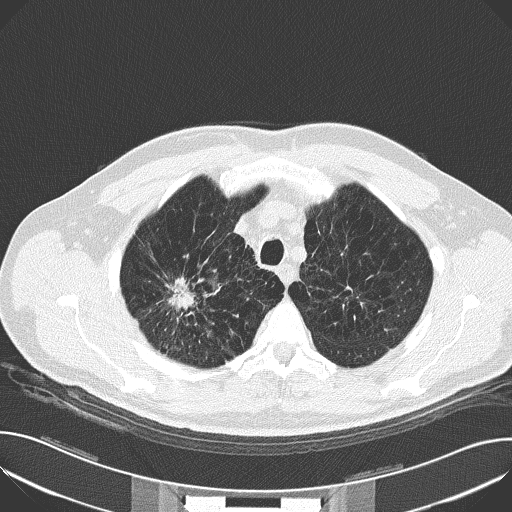
Axial slice from a low-dose chest CT screening exam; baseline annual screen; lung window (W 1500 / L -600 HU); 2 mm slice thickness; 120 kVp; slice 27 of 159 in the series; 512 × 512 image matrix, field of view 380 × 380 mm. Male participant, aged 59 years at enrolment.
• Expert-annotated lung lesion, bounding box (x1, y1, x2, y2) in pixels: (154, 260, 216, 327).
• The screening reader recorded 4 non-calcified nodules or masses ≥4 mm on this exam (right upper lobe, left upper lobe, right upper lobe, left upper lobe); which of them this box marks is not recorded.
• Official screen result: positive, change unspecified: nodule(s) >= 4 mm or enlarging nodule(s), mass(es), or other non-specific abnormalities suspicious for lung cancer.
• Participant outcome: lung cancer diagnosed 44 days after this screen — squamous cell carcinoma, NOS, right upper lobe, moderately differentiated (G2), stage IA (AJCC 6th edition), 30 mm at pathology.